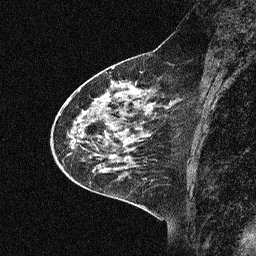
Breast MRI (dynamic contrast-enhanced), one sagittal slice; position 24 of 64 along the scan axis; dynamic contrast-enhanced study with each time point stored as its own series, time point 2 of 3 at this slice position (early post-contrast, ordered by acquisition time); 1.5 T; TE 4.5 ms, TR 11 ms; 256 × 256 image matrix, field of view 200 × 200 mm. Female patient, age 46 years. Case-level facts recorded for this patient, not image findings: setting: breast cancer imaged before/during neoadjuvant chemotherapy; receptor status: HER2-positive.
Structures marked on this image (semi-automatic segmentation, software-assisted and operator-edited):
- analysis volume of interest (the breast-tissue region the enhancement analysis was run in; not a lesion): box from (x=46, y=51) to (x=180, y=169) px
- tumour enhancement mask (voxels above the 90 % enhancement threshold inside the analysis volume of interest): (x=87, y=99)–(x=99, y=167)